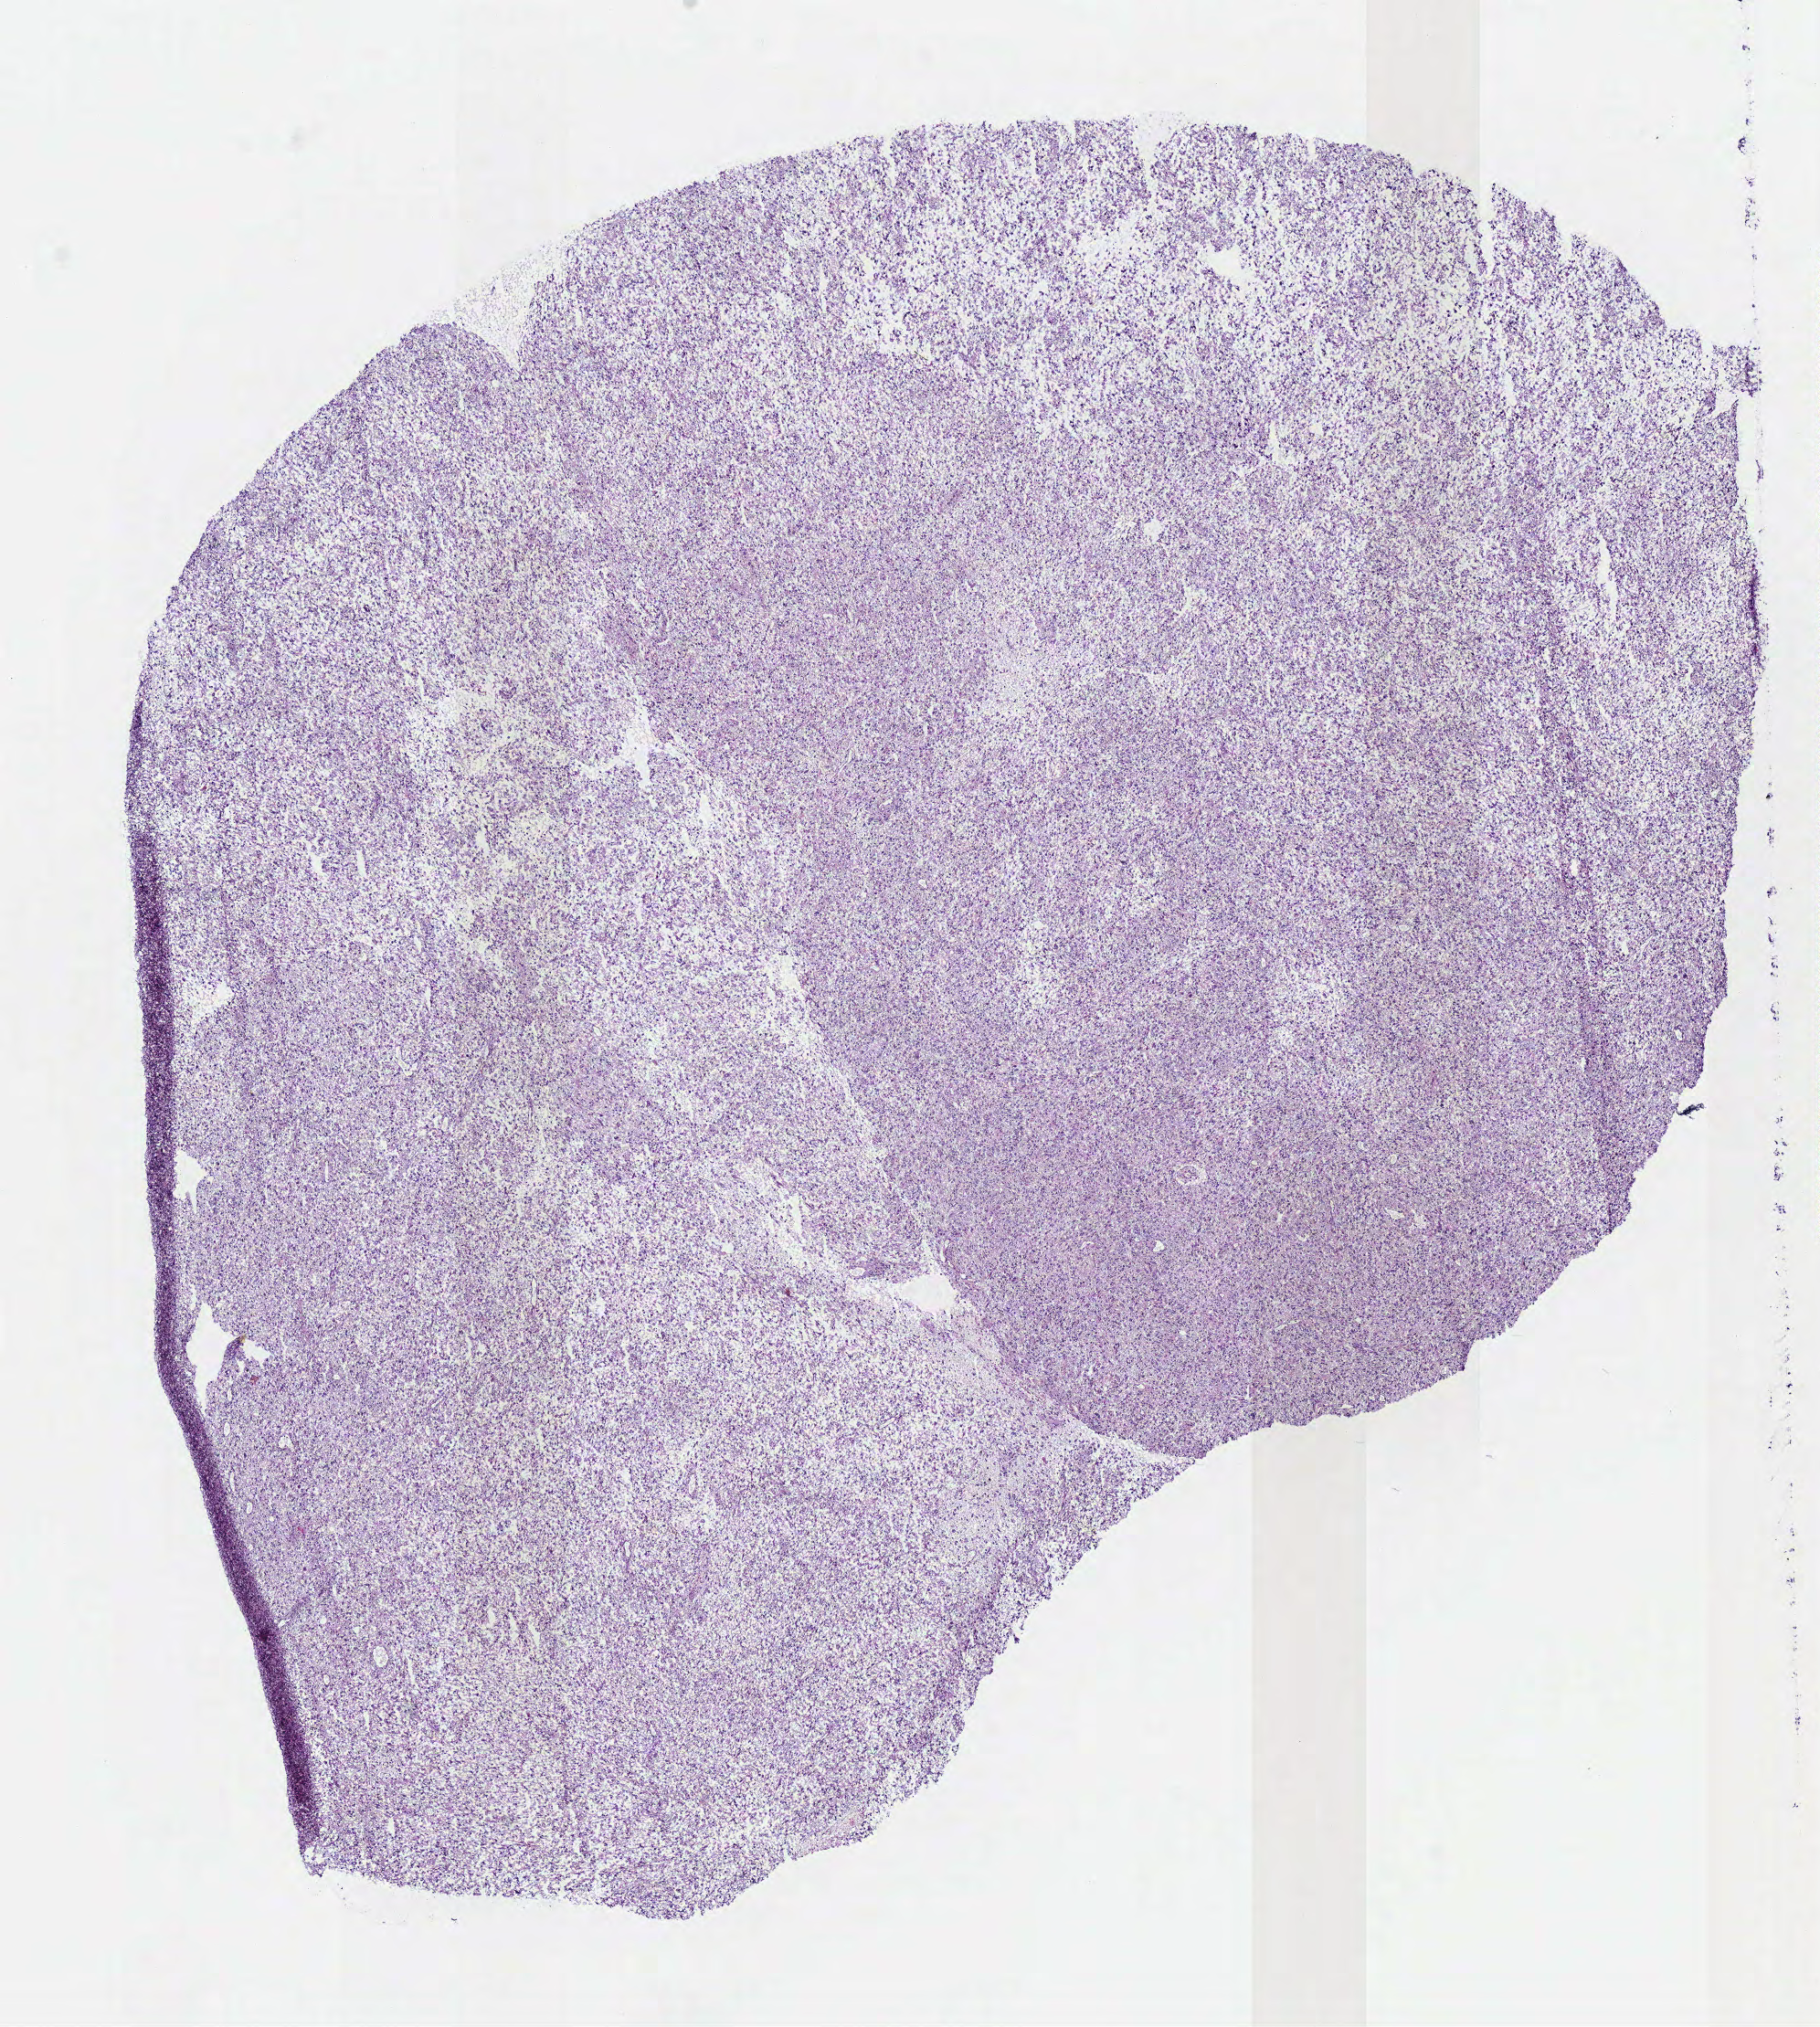
Digitized H&E tissue section (whole slide), low-resolution overview of the scanned area, about 7.8 x 8.7 mm. Frozen section from the bottom of the tissue portion. Sample: primary tumour, brain. Female, age 60 years at initial diagnosis. Pathologist review of this section (percent, as recorded): tumour cells 100%, tumour nuclei 75%.
Pathologic diagnosis: Astrocytoma, anaplastic (cerebrum).